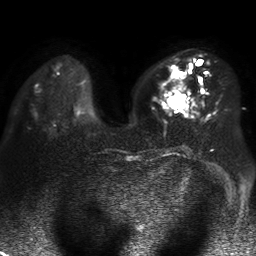
Breast MRI, one axial slice. Diffusion-weighted series; image 2 of 4 stored at this slice position (different b-values; order by instance number). 1.5 T. 4 mm slice thickness. 256 × 256 image matrix. Female patient.
Outlined on this slice (outlined manually by an expert reader):
- tumour on diffusion-weighted imaging: bounding box (x1, y1, x2, y2) in pixels: (169, 72, 186, 109)